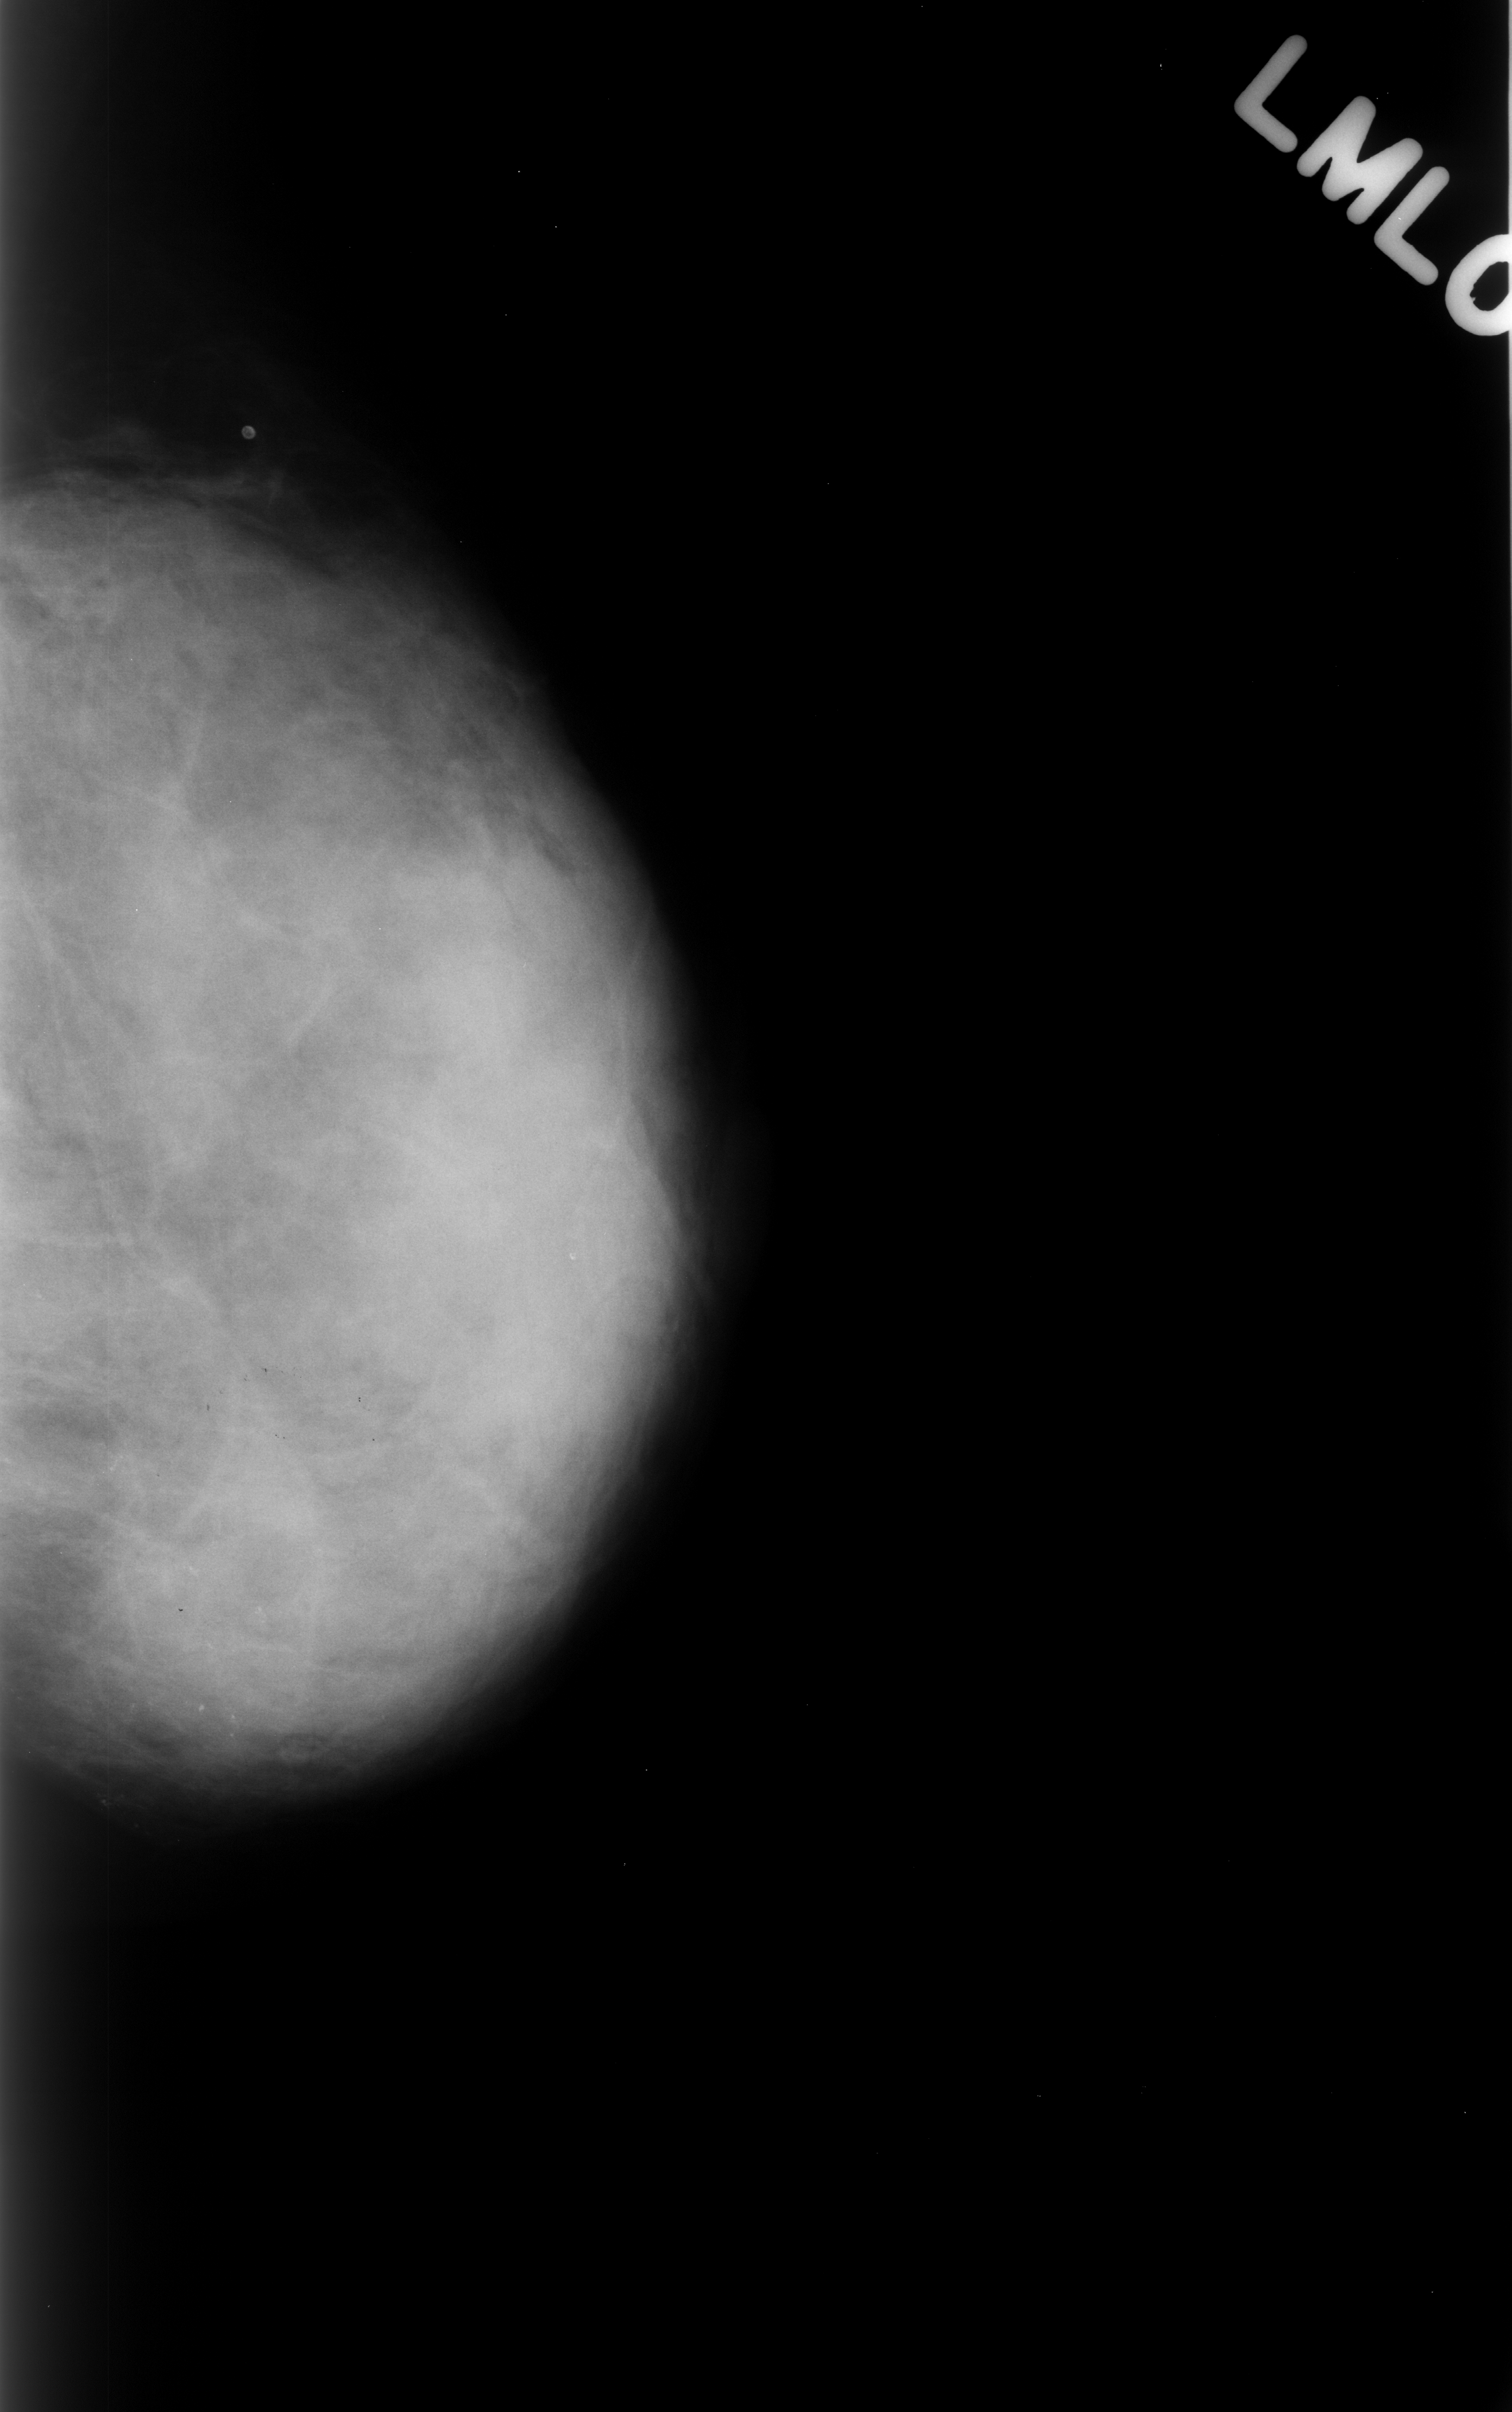
Scanned film-screen mammogram, left breast, MLO view.
Calcifications, morphology pleomorphic, distribution segmental; BI-RADS assessment category 4; subtlety rating 3 on a 1 (subtle) to 5 (obvious) scale; pathology result (as recorded, not read from the image): benign.